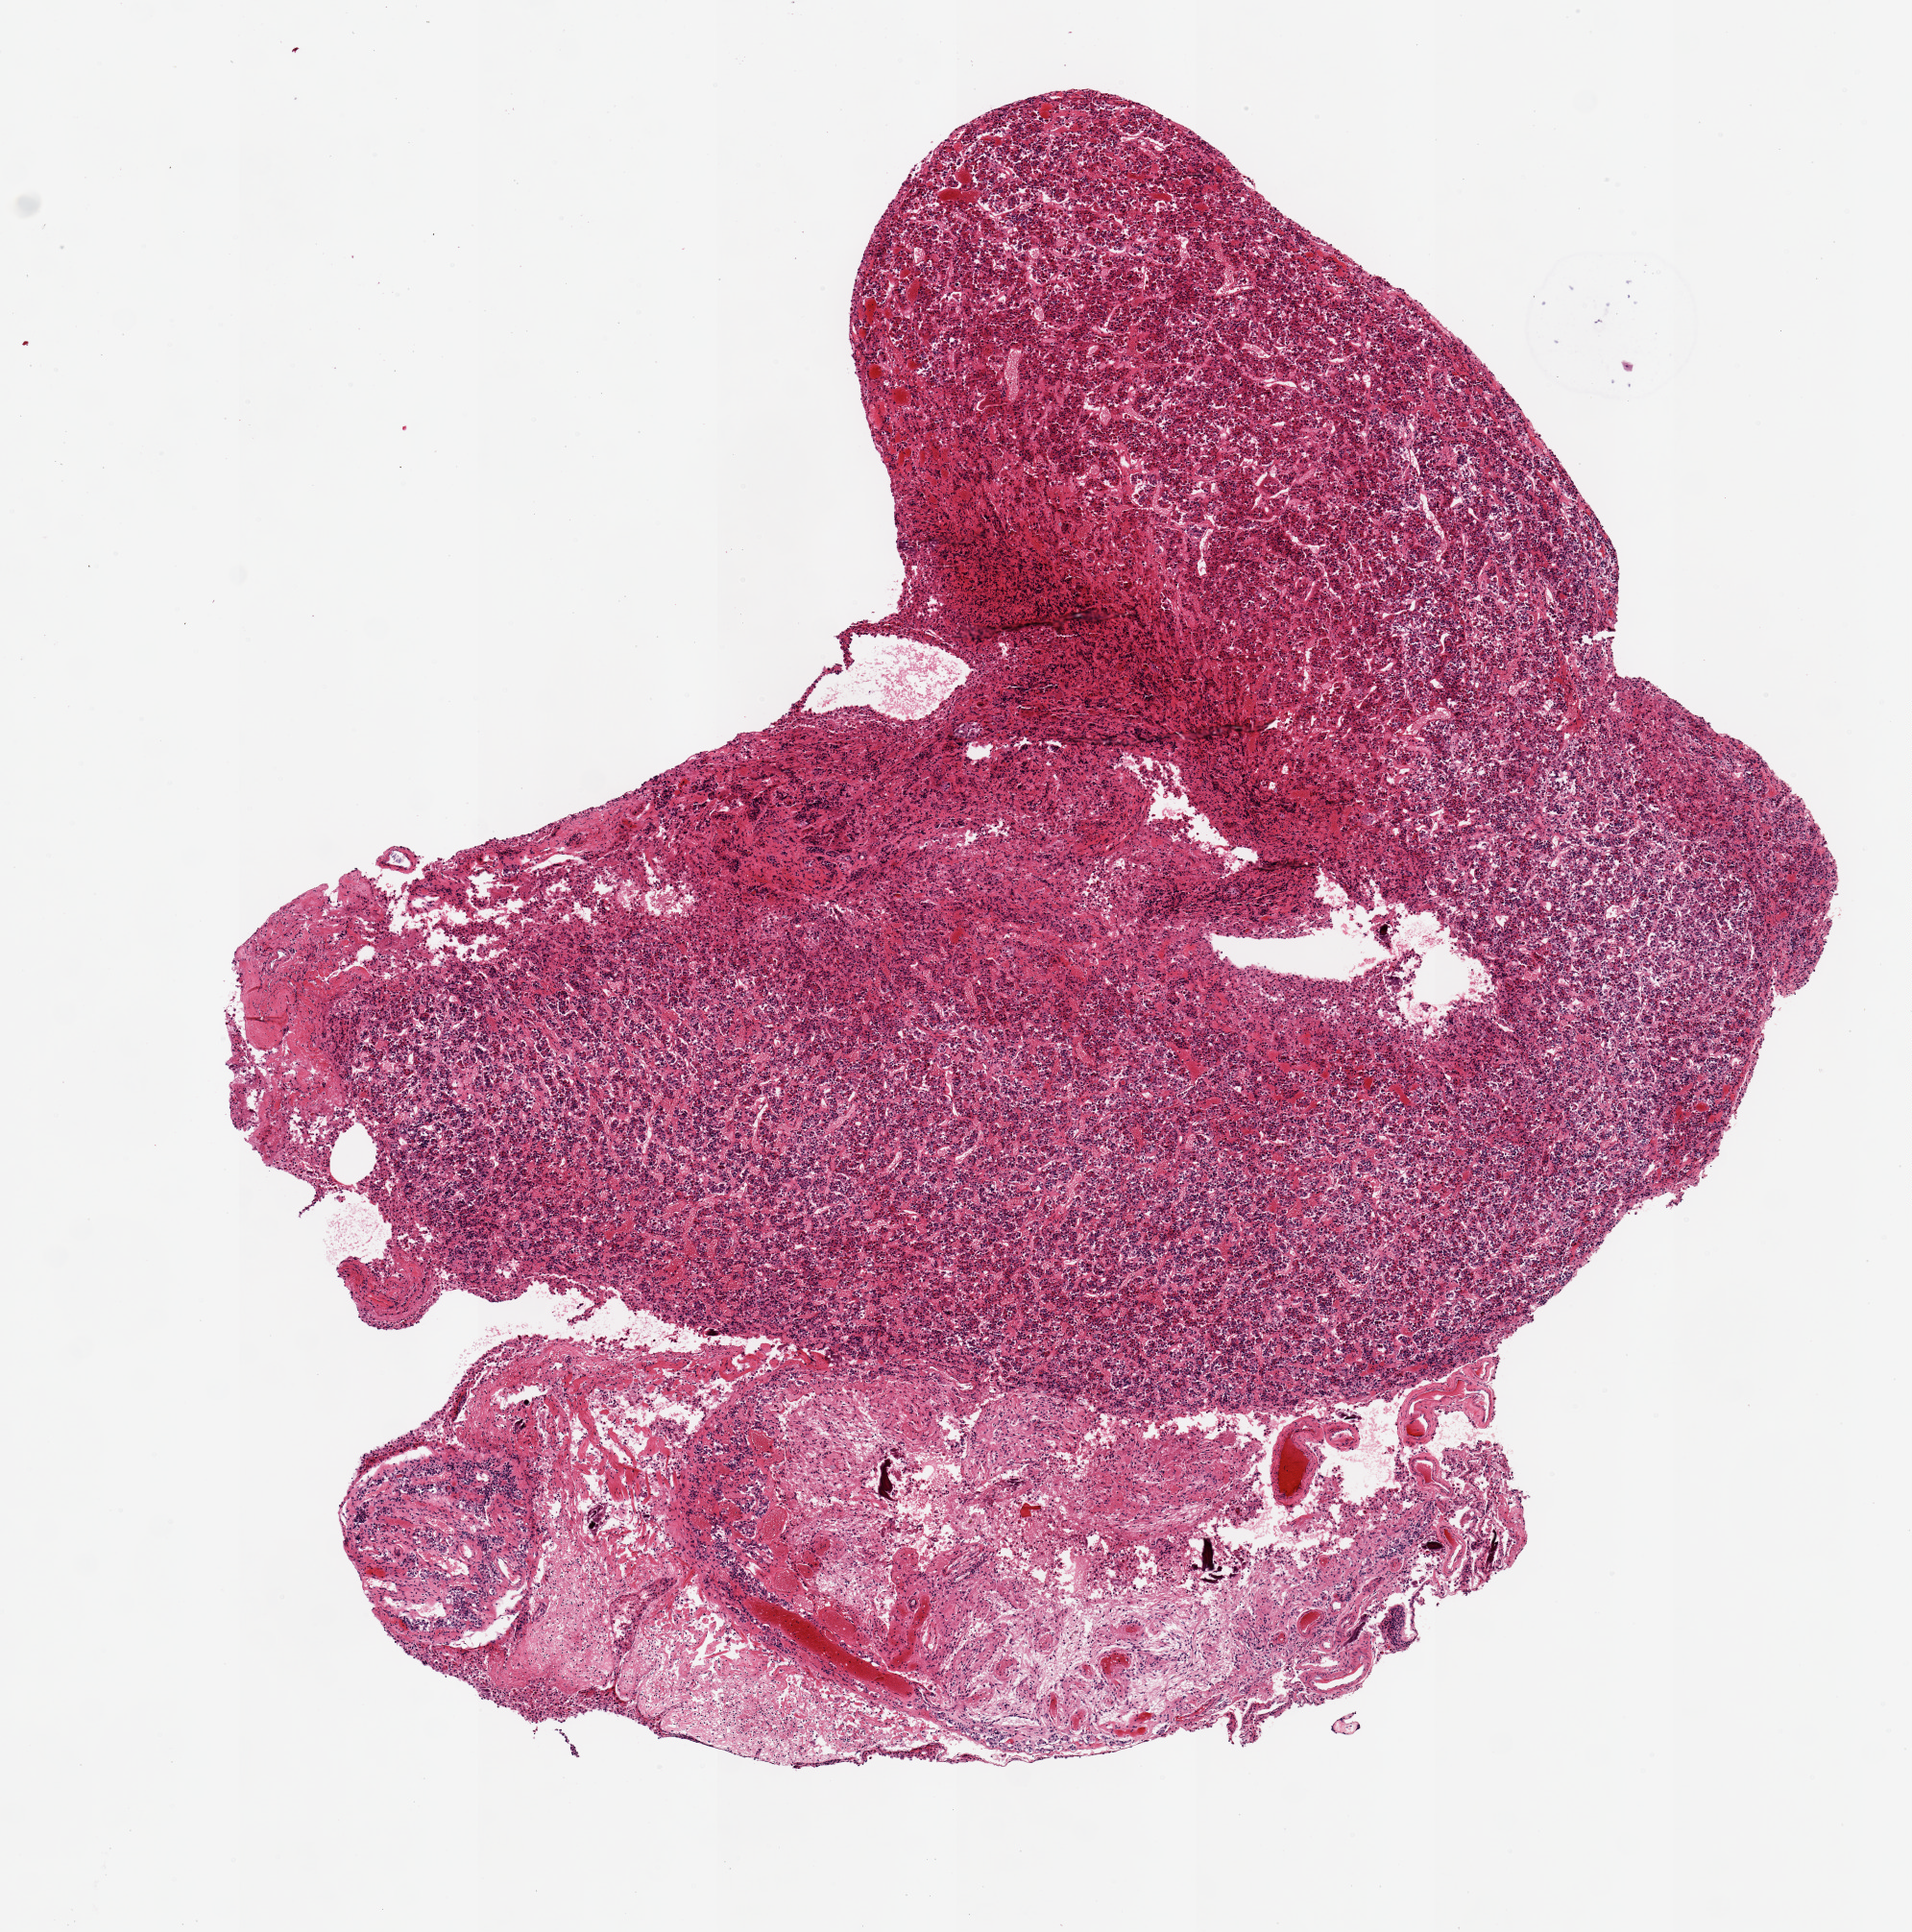
Whole-slide image, haematoxylin and eosin stain, brightfield — whole scanned area (about 7.9 x 8.0 mm, from a 20x scan) shown as a low-resolution overview; PAXgene-fixed paraffin-embedded (PFPE) section; section of pituitary (target tissue); tissue donor sample. Donor: male.
Review note (as recorded): 1 pieces ~6x6mm, adherent focus fibrous tissue encicled.